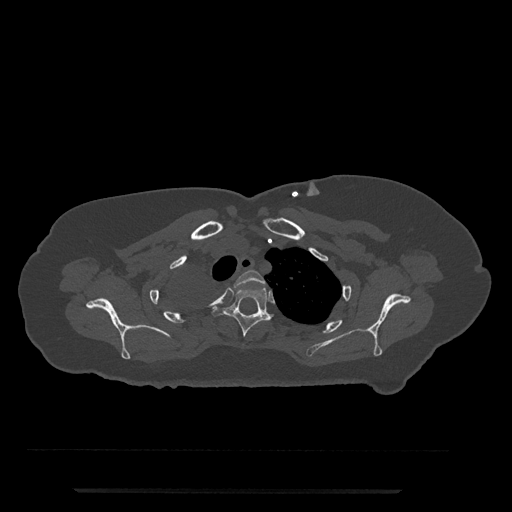
CT including the spine, one axial slice; slice 637 of 797 in the series (ordered by position); reconstruction kernel Br40s/3; 120 kVp; bone window (W 1800 / L 400 HU); 0.5 mm slice thickness; 512 × 512 image matrix, field of view 440 × 440 mm. Female patient, age 51 years. From the clinical record (not read from this slice): primary cancer: neuro; vertebrae with lytic lesions (as recorded): T8.
Outlined on this slice (semi-automatic segmentation, software-assisted and operator-edited):
- T2 vertebra: bounding box <234,270,265,288> (left, top, right, bottom; pixels)
- T3 vertebra: <213,287,271,337>